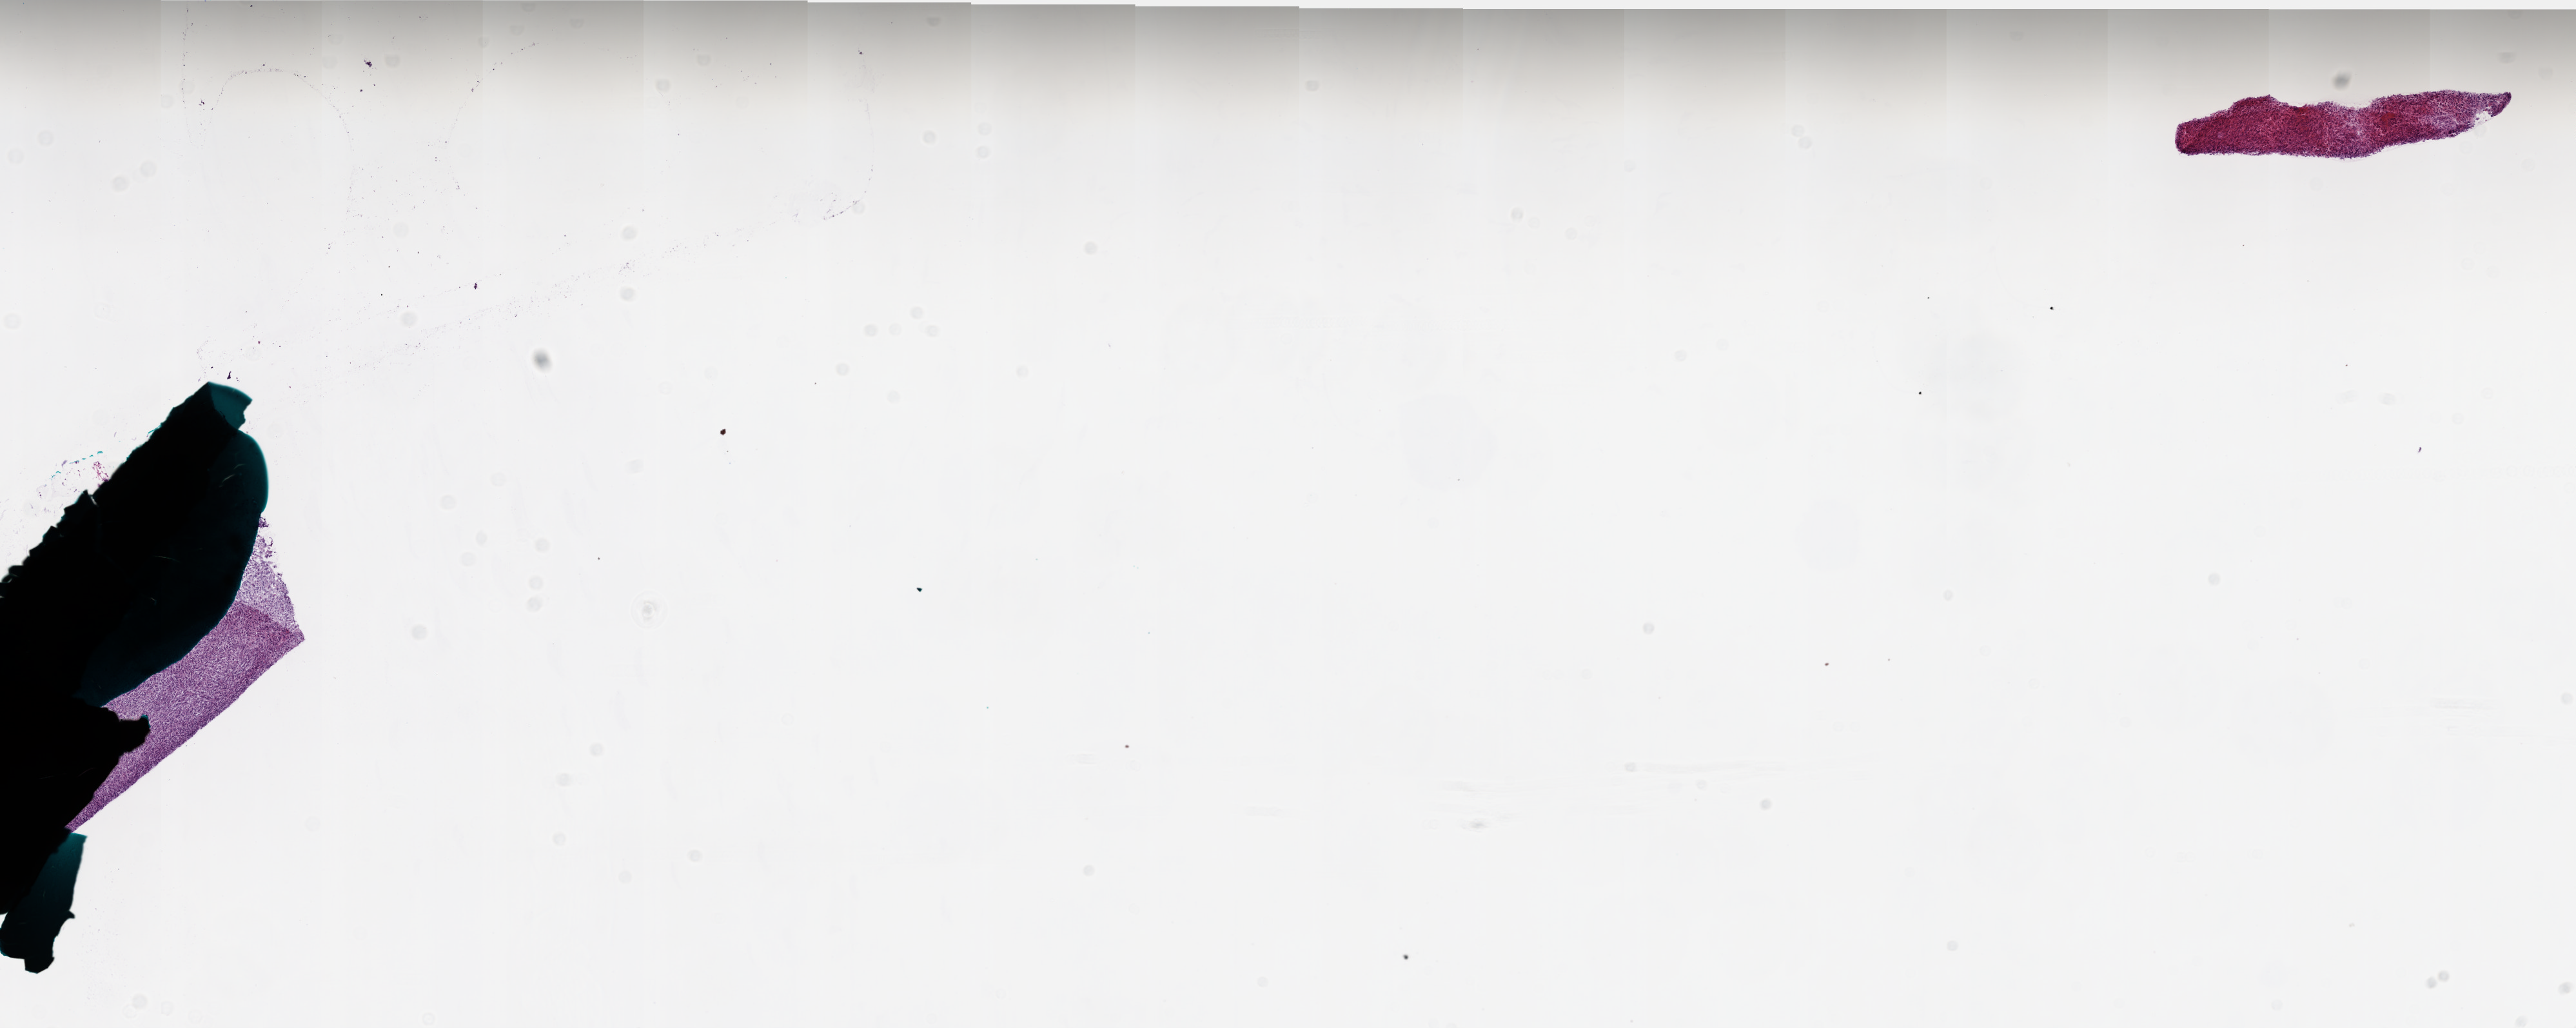
H&E-stained whole-slide image, low-resolution overview of the scanned area, about 16.0 x 6.4 mm, frozen section from the bottom of the tissue portion, sample: primary tumour, brain. Male, age 40 years at initial diagnosis. Pathologist review of this section (percent, as recorded): tumour cells 100%, tumour nuclei 98%.
Histologic diagnosis: Glioblastoma.